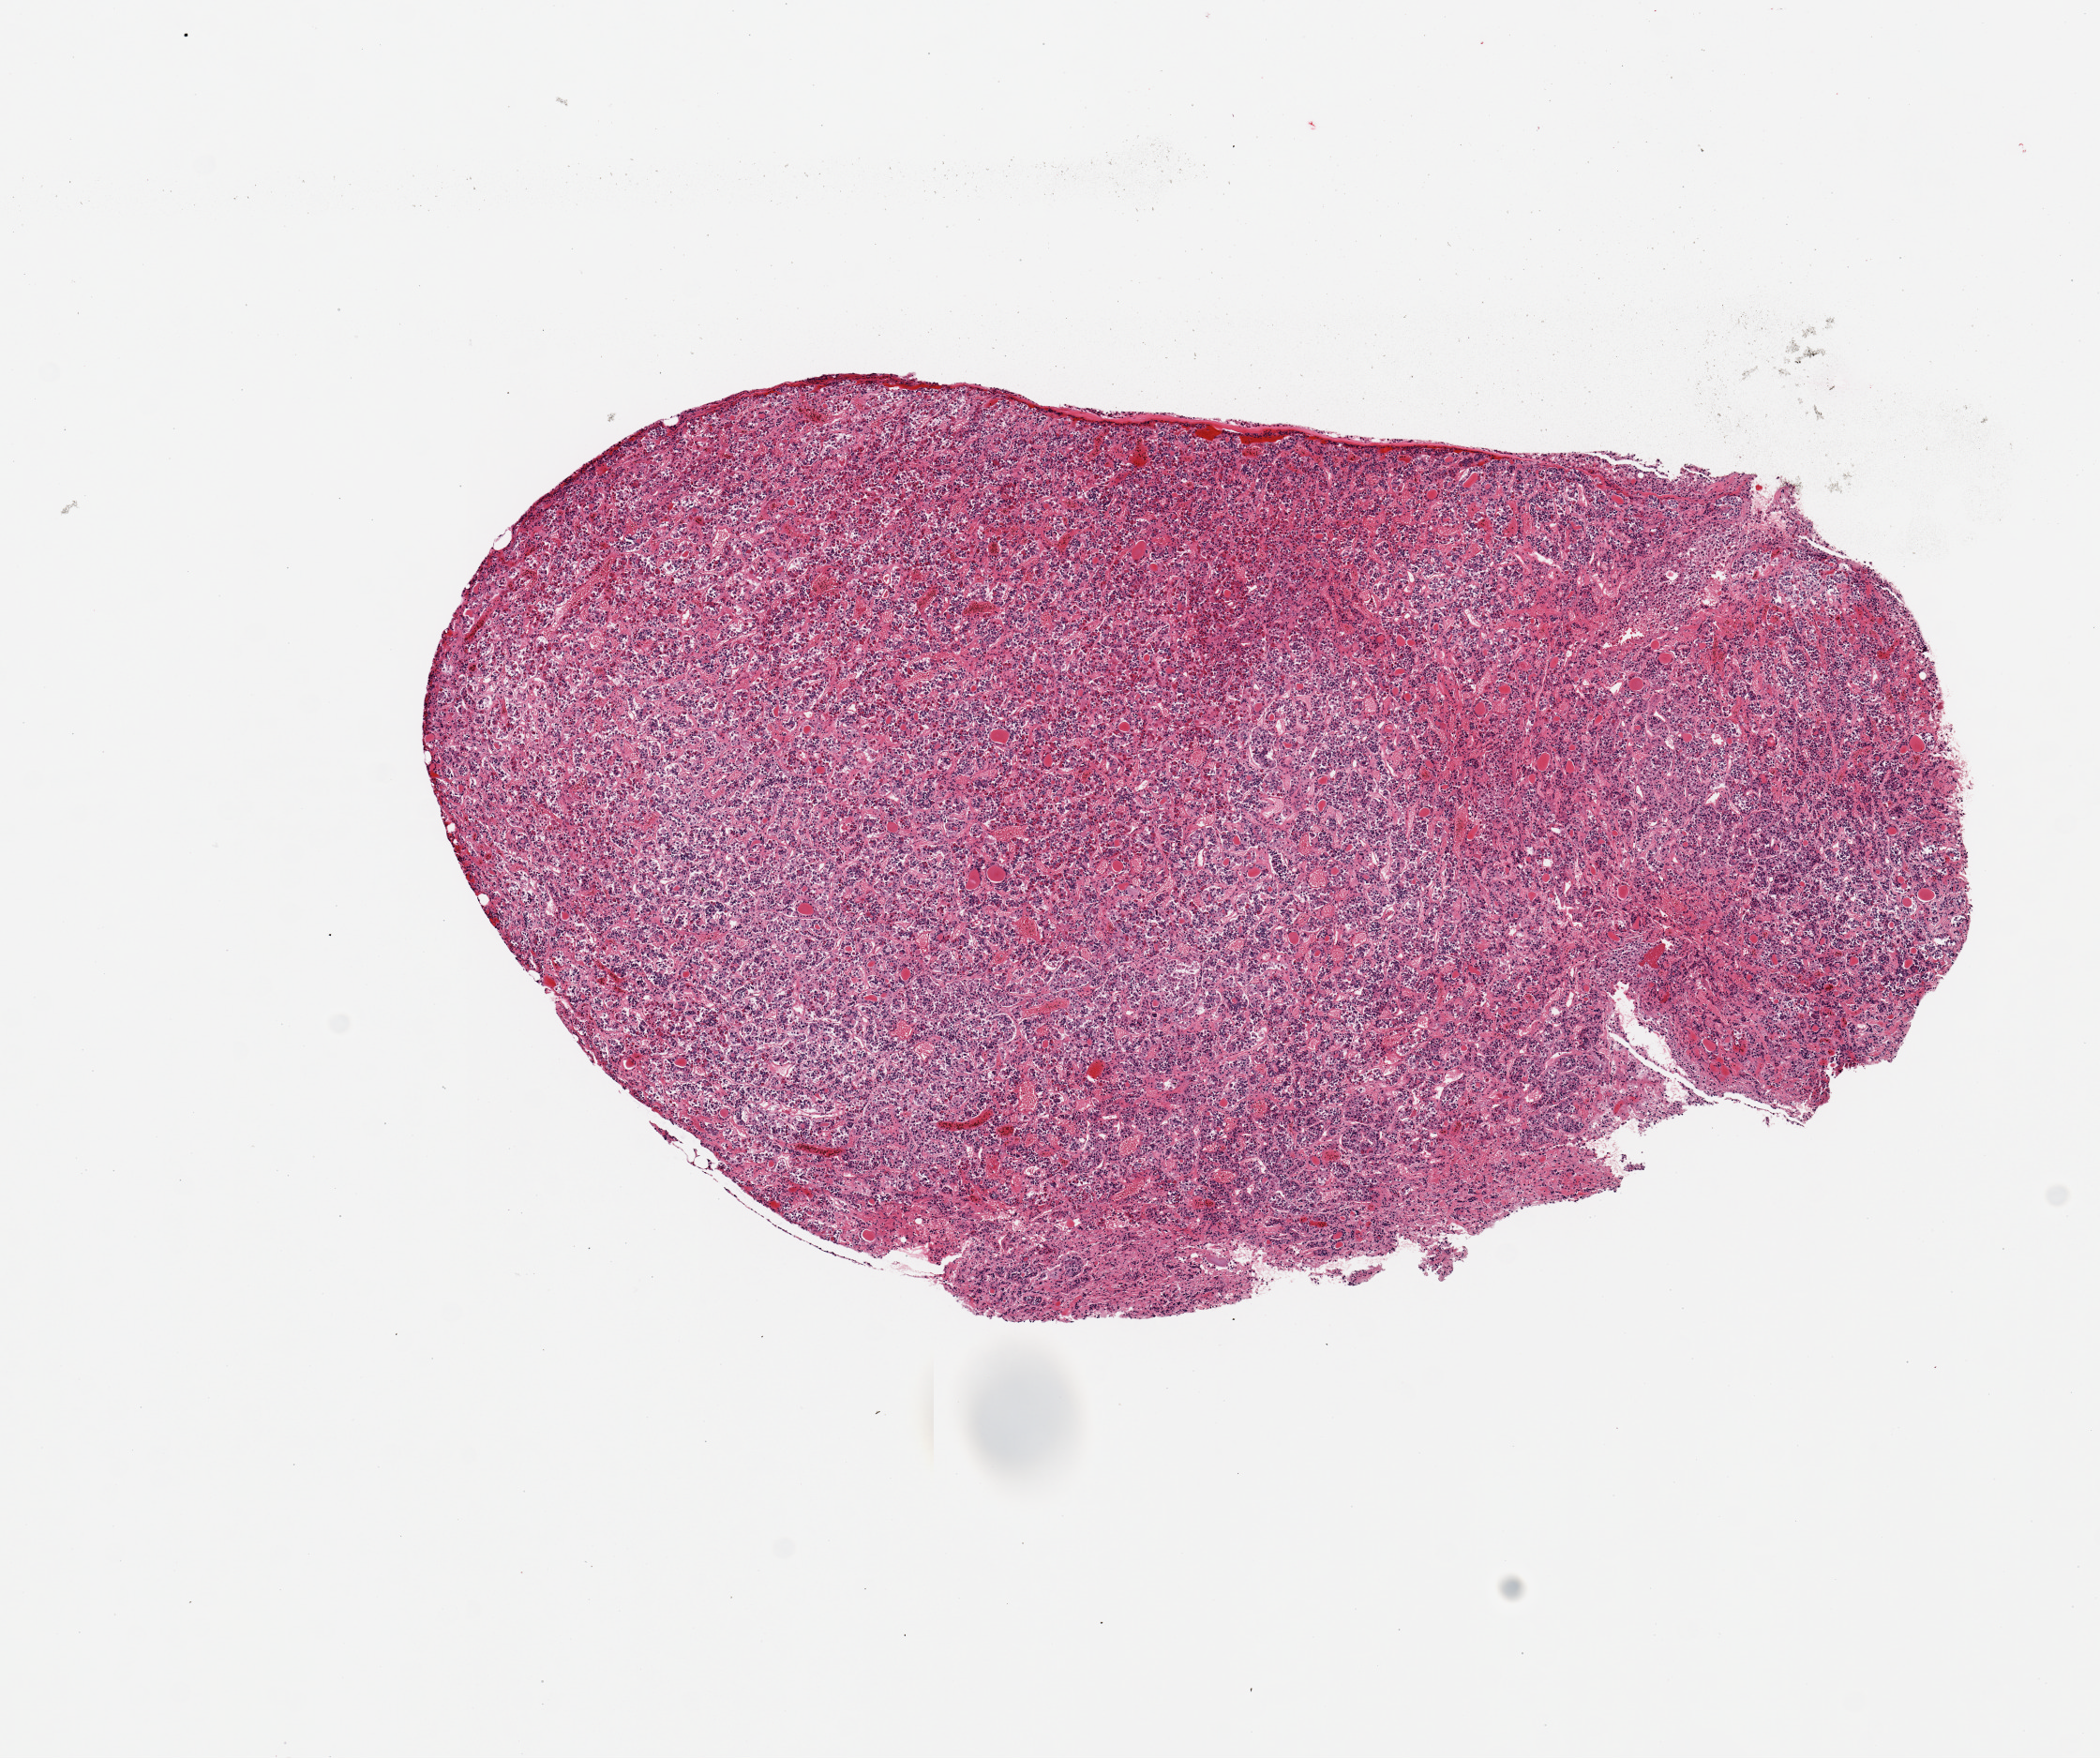
H&E whole-slide image — a low-resolution overview of the entire scanned area, about 8.9 x 7.4 mm, PAXgene-fixed paraffin-embedded (PFPE) section, sampled site (target tissue): pituitary, donor tissue sample. Donor sex: female.
Review note (as recorded): 1 piece.